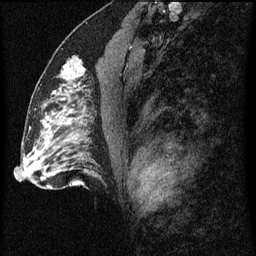
Breast MRI (dynamic contrast-enhanced), one sagittal slice. Position 39 of 60 along the scan axis. Dynamic contrast-enhanced series, image 2 of 3 at this slice position (ordered by acquisition). 1.5 T. TE 4.2 ms, TR 8 ms. 256 × 256 image matrix, field of view 180 × 180 mm. Female patient, age 51 years.
Structures marked on this image (semi-automatically segmented with operator editing):
- analysis volume of interest (the breast-tissue region the enhancement analysis was run in; not a lesion): bounding box (x1, y1, x2, y2) in pixels: (54, 50, 93, 103)
- tumour enhancement mask (voxels above the 70 % enhancement threshold inside the analysis volume of interest): (54, 68, 81, 95)